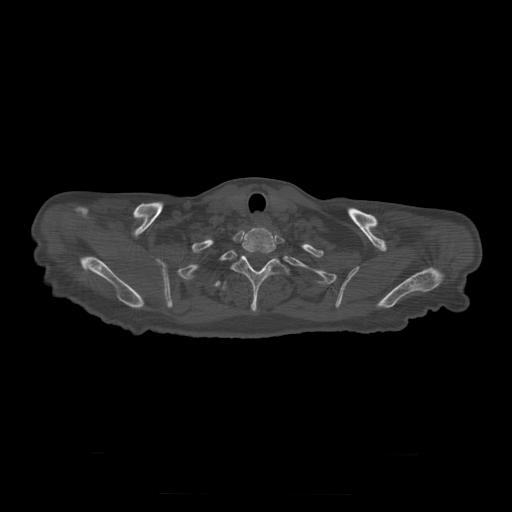
CT including the spine, one axial slice; 120 kVp; bone window (W 1800 / L 400 HU); 512 × 512 image matrix, field of view 510 × 510 mm. Patient age 73 years. Case-level facts recorded for this patient, not image findings: primary cancer: prostate.
Structures marked on this image (semi-automatic segmentation, software-assisted and operator-edited):
- T1 vertebra: bounding box (x1, y1, x2, y2) in pixels: (238, 231, 276, 254)
- T2 vertebra: (232, 254, 290, 312)
- T3 vertebra: (222, 282, 230, 291)